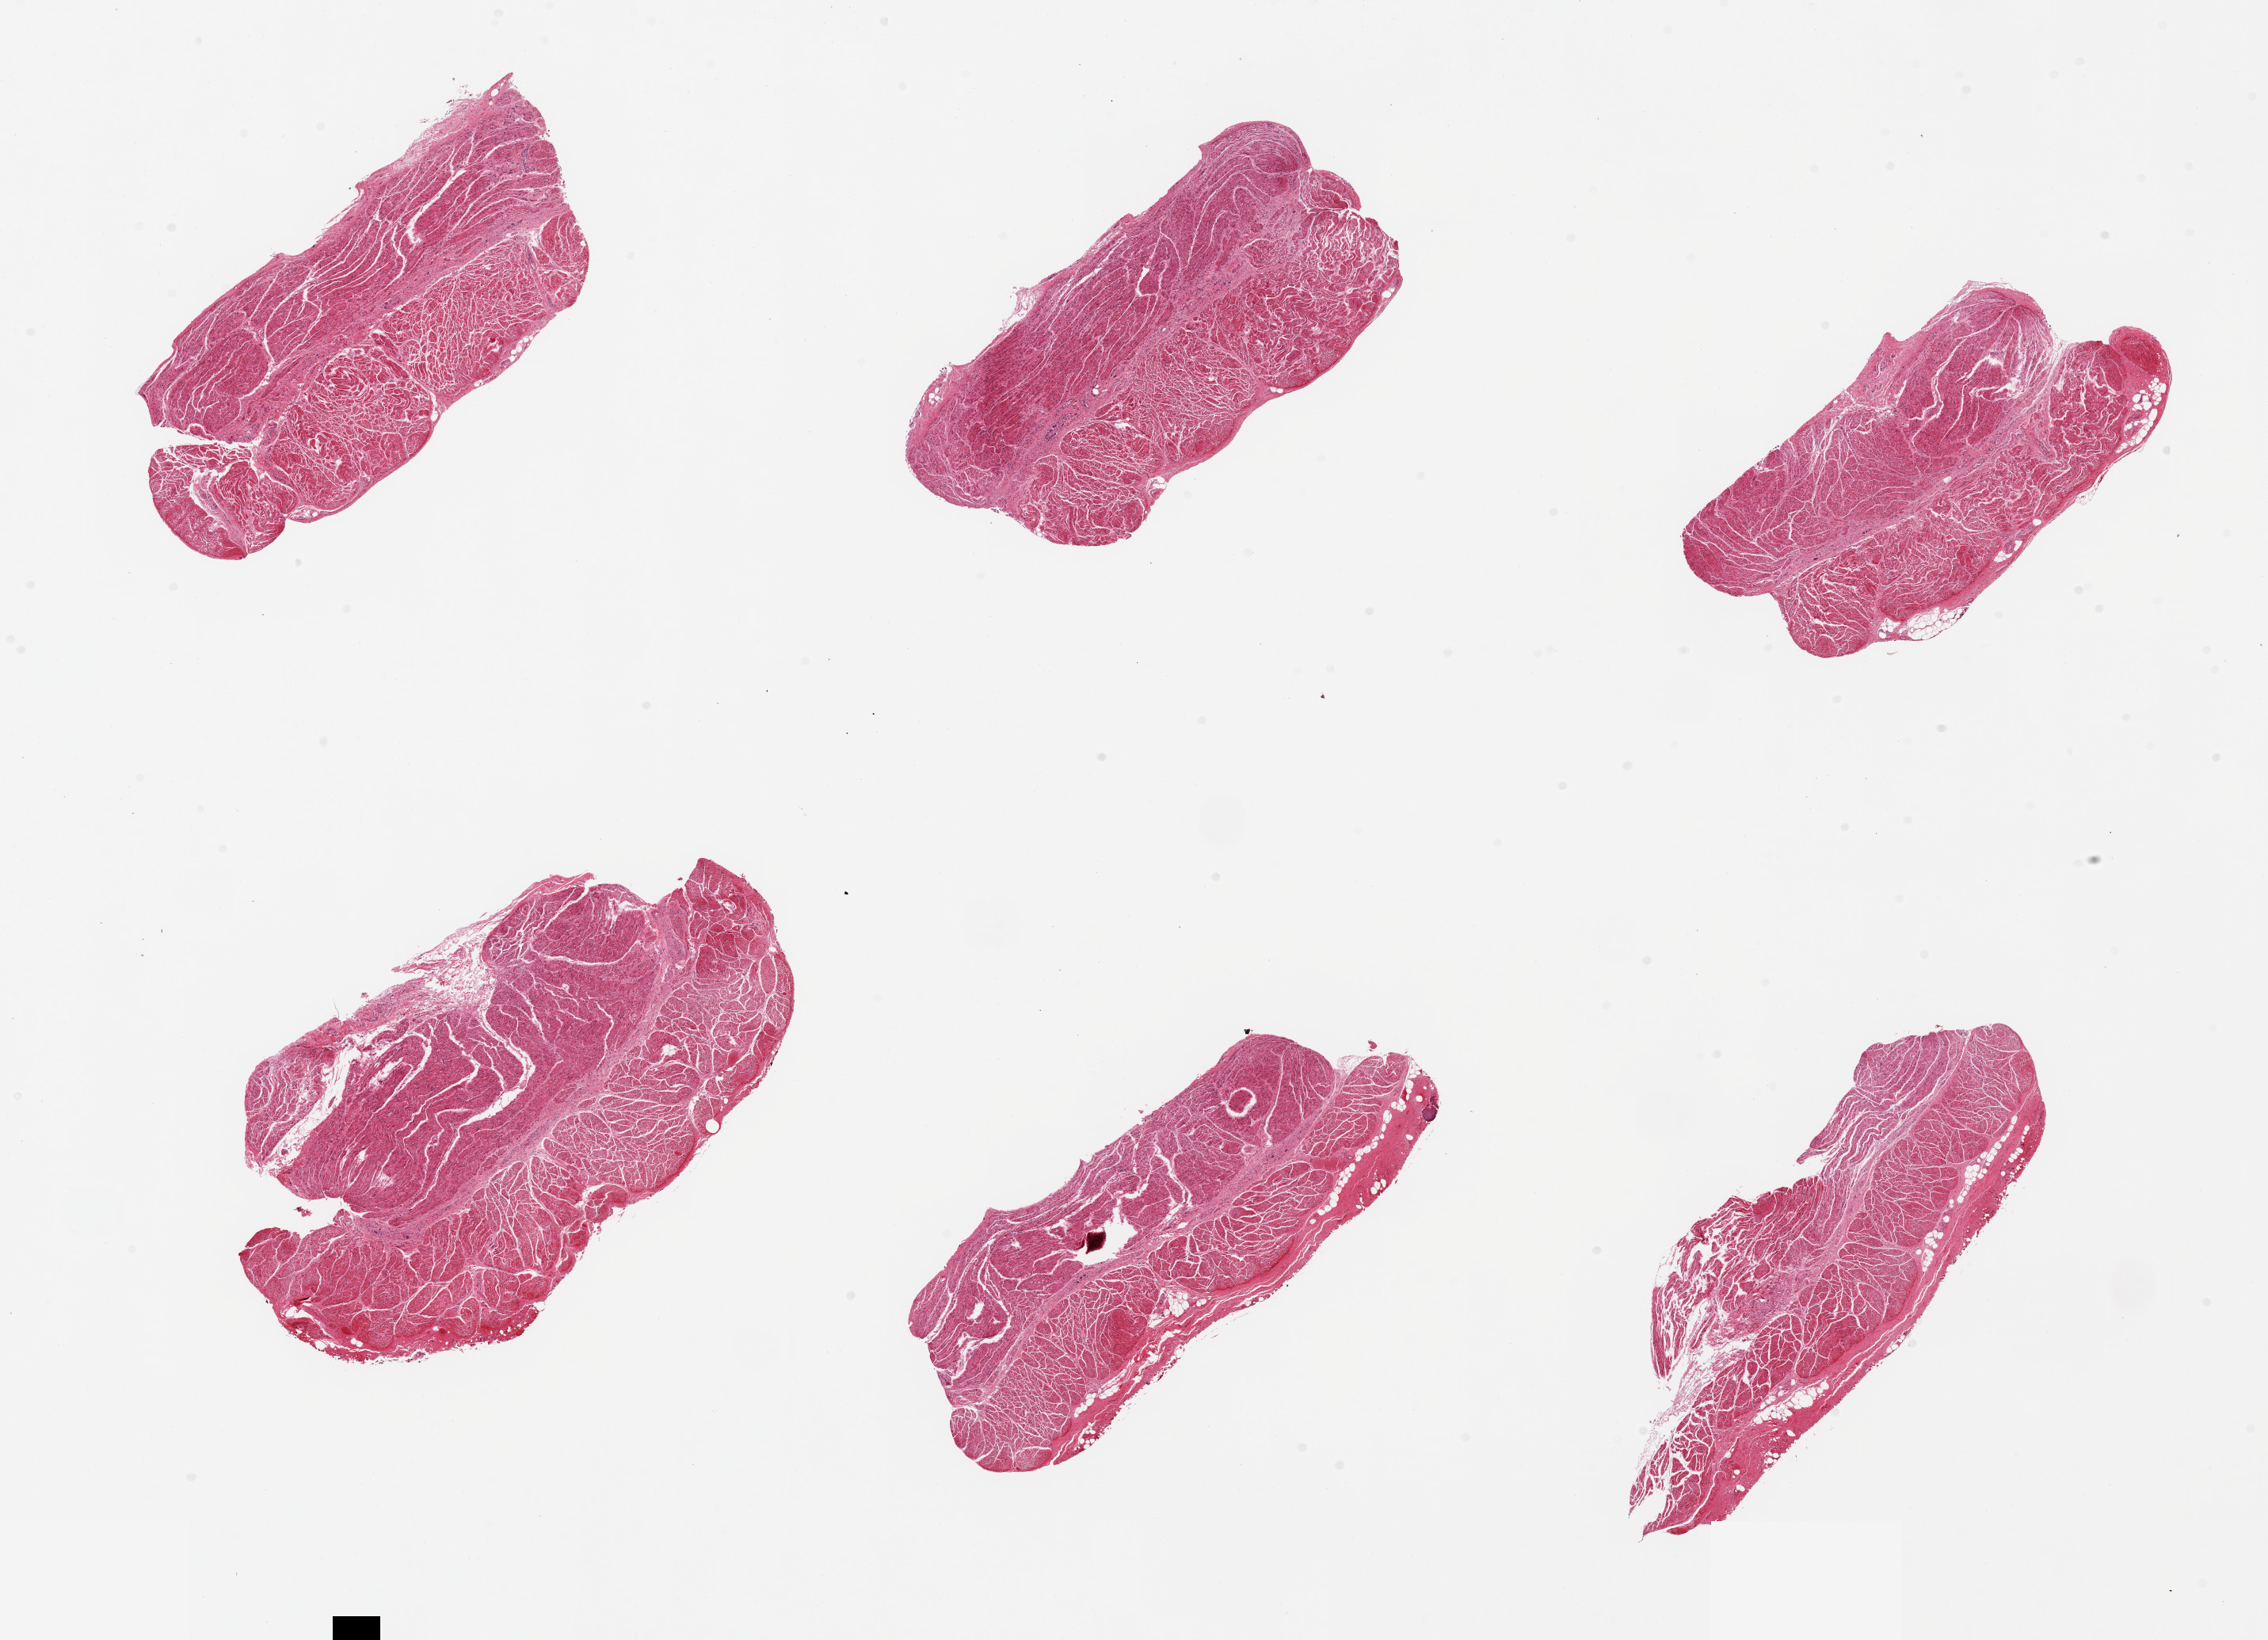
Digitized H&E-stained section, brightfield, whole scanned area (about 22.6 x 16.4 mm, from a 20x scan) shown as a low-resolution overview; PAXgene-fixed, paraffin-embedded tissue; section of gastroesophageal junction (target tissue); tissue donor sample. Donor: male.
- reviewer comment on this tissue sample: 6 pieces; well trimmed